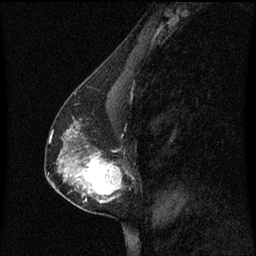
Breast MRI (dynamic contrast-enhanced), one sagittal slice. Position 33 of 60 along the scan axis. Dynamic contrast-enhanced series, image 2 of 3 at this slice position (ordered by acquisition). 1.5 T. TE 4.2 ms, TR 8.4 ms. 2 mm slice thickness. 256 × 256 image matrix. Female patient, age 40 years. From the clinical record (not read from this slice): setting: breast cancer imaged before/during neoadjuvant chemotherapy; receptor status: triple-negative.
Structures marked on this image (semi-automatically segmented with operator editing):
- analysis volume of interest (the breast-tissue region the enhancement analysis was run in; not a lesion): bounding box (x1, y1, x2, y2) in pixels: (60, 104, 129, 215)
- tumour enhancement mask (voxels above the 70 % enhancement threshold inside the analysis volume of interest): (76, 132, 123, 203)